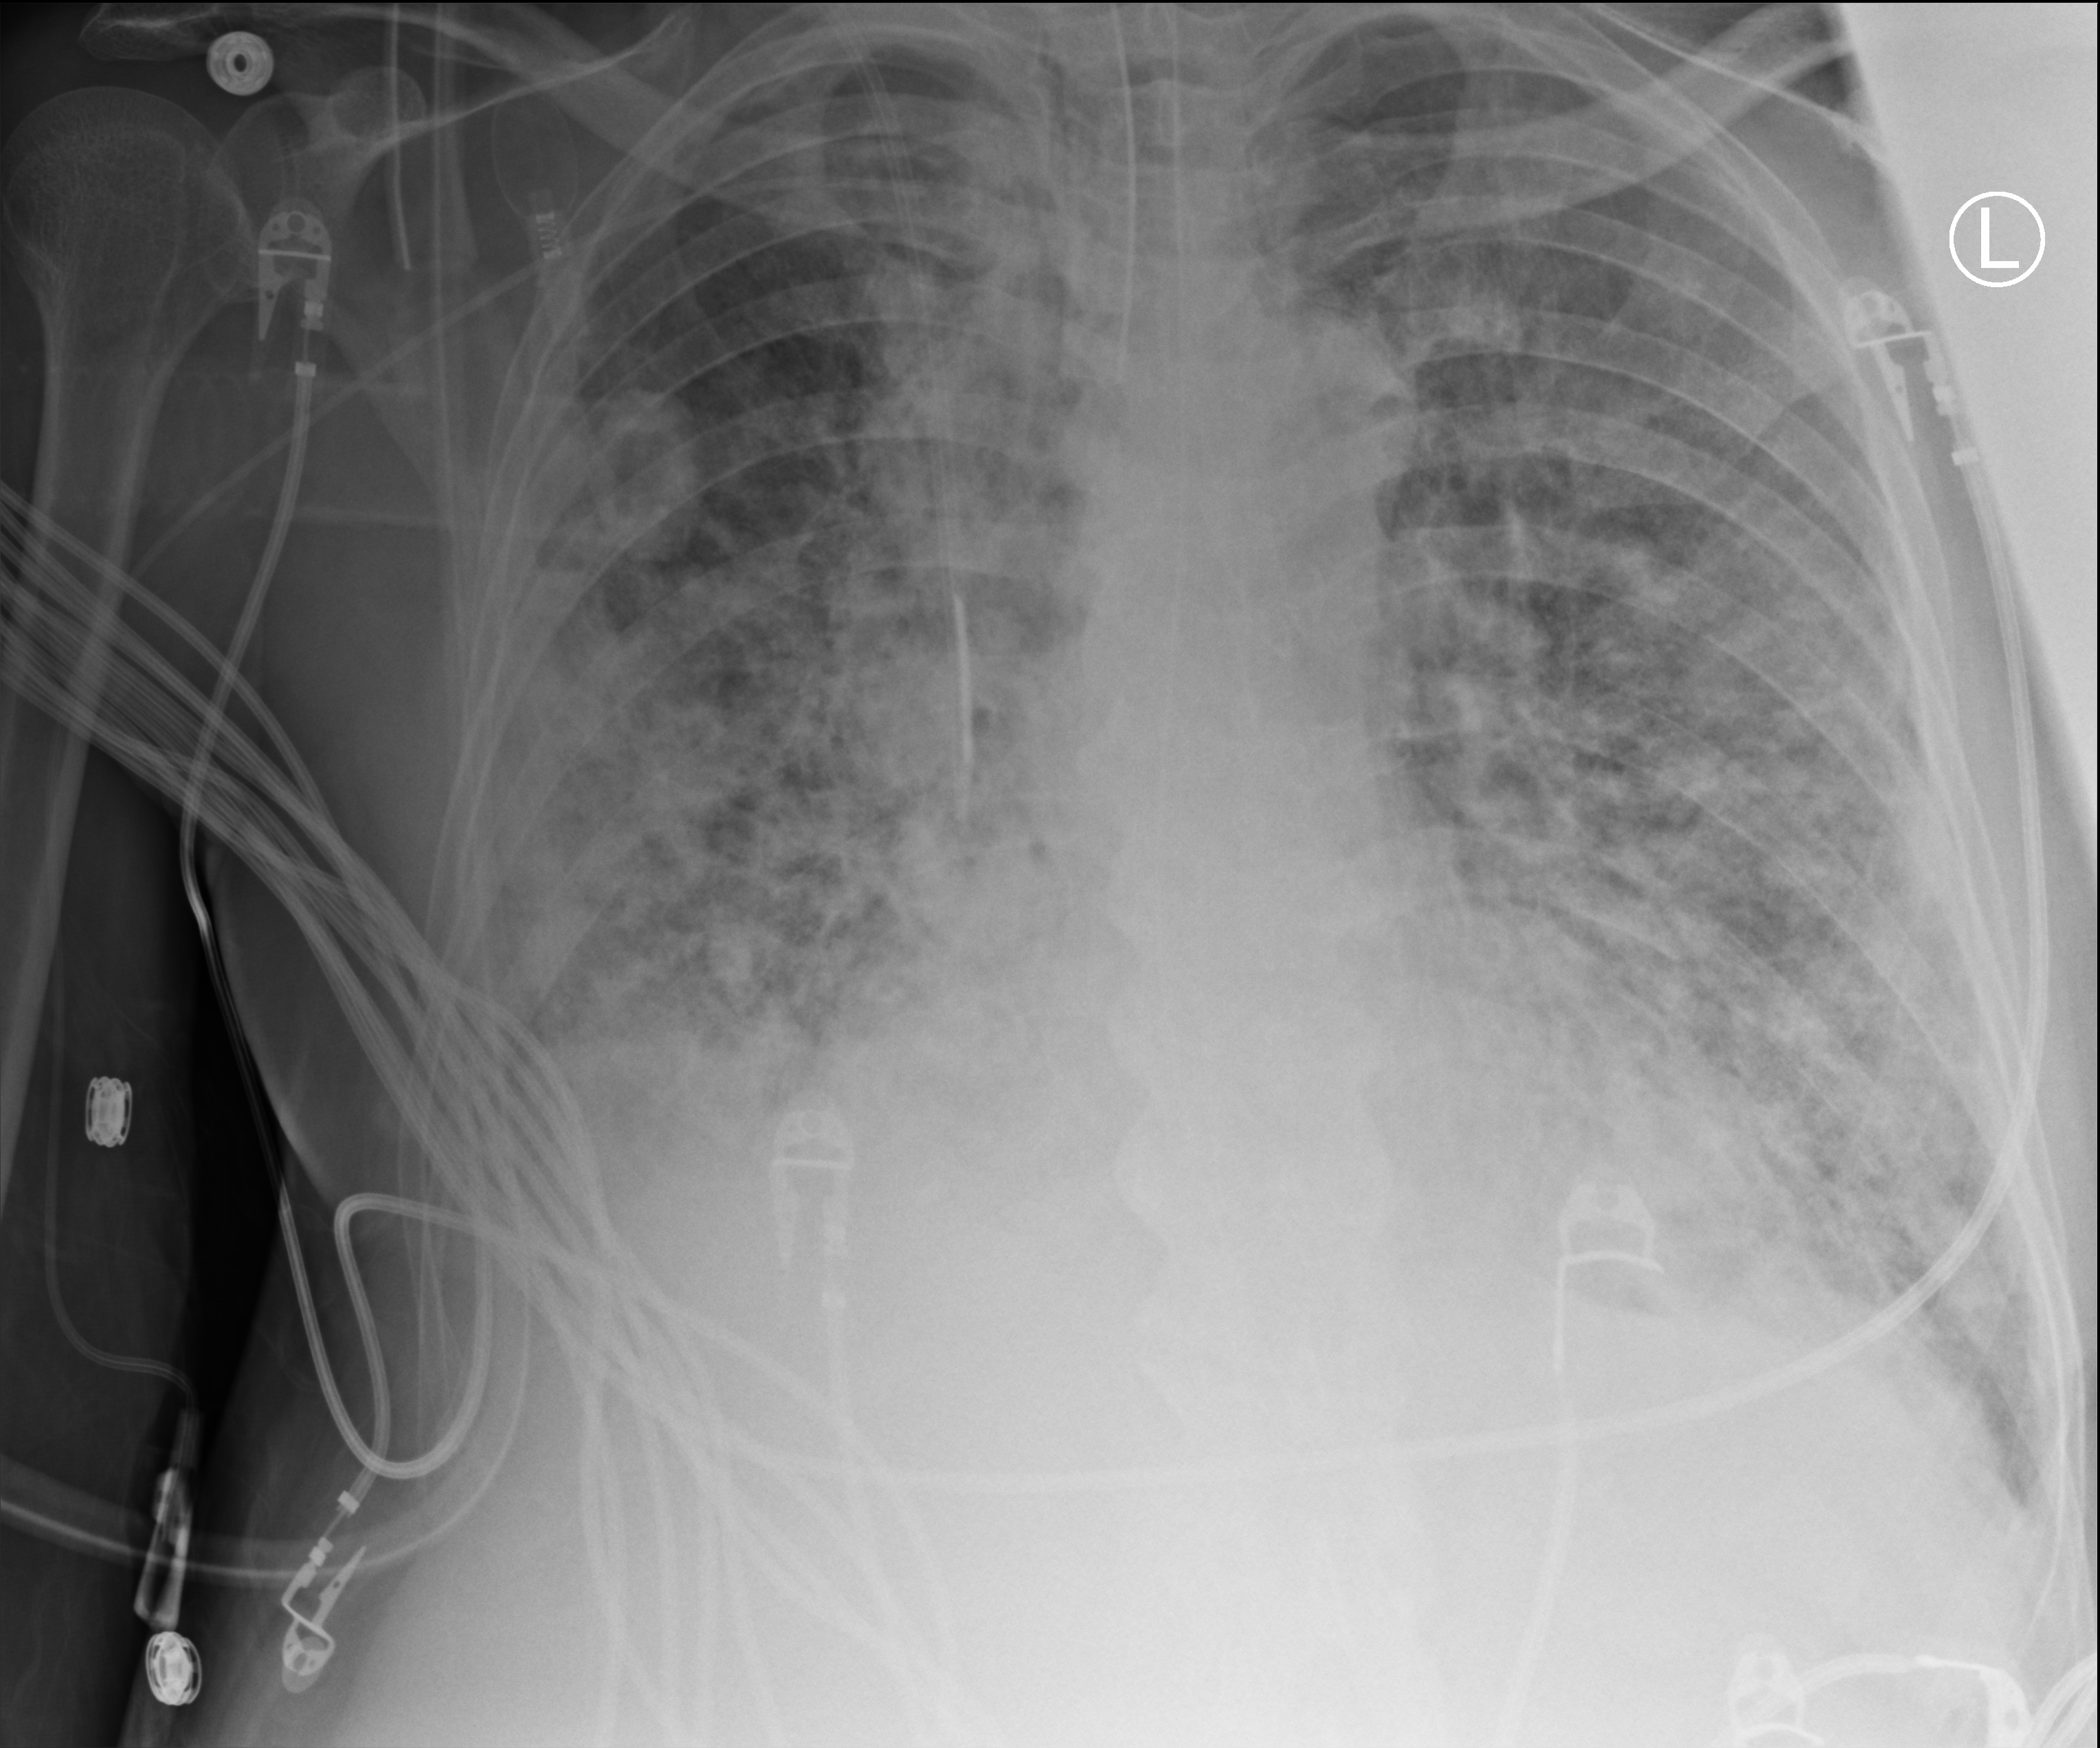
Bedside chest radiograph (computed radiography), anteroposterior (AP) projection. Patient hospitalised with COVID-19; male, aged 60–74 years.
From the hospital-stay record, not from the radiograph (when in the stay this image was taken is not recorded):
- diabetes (admission record): no
- admitted to intensive care during this hospital stay: yes